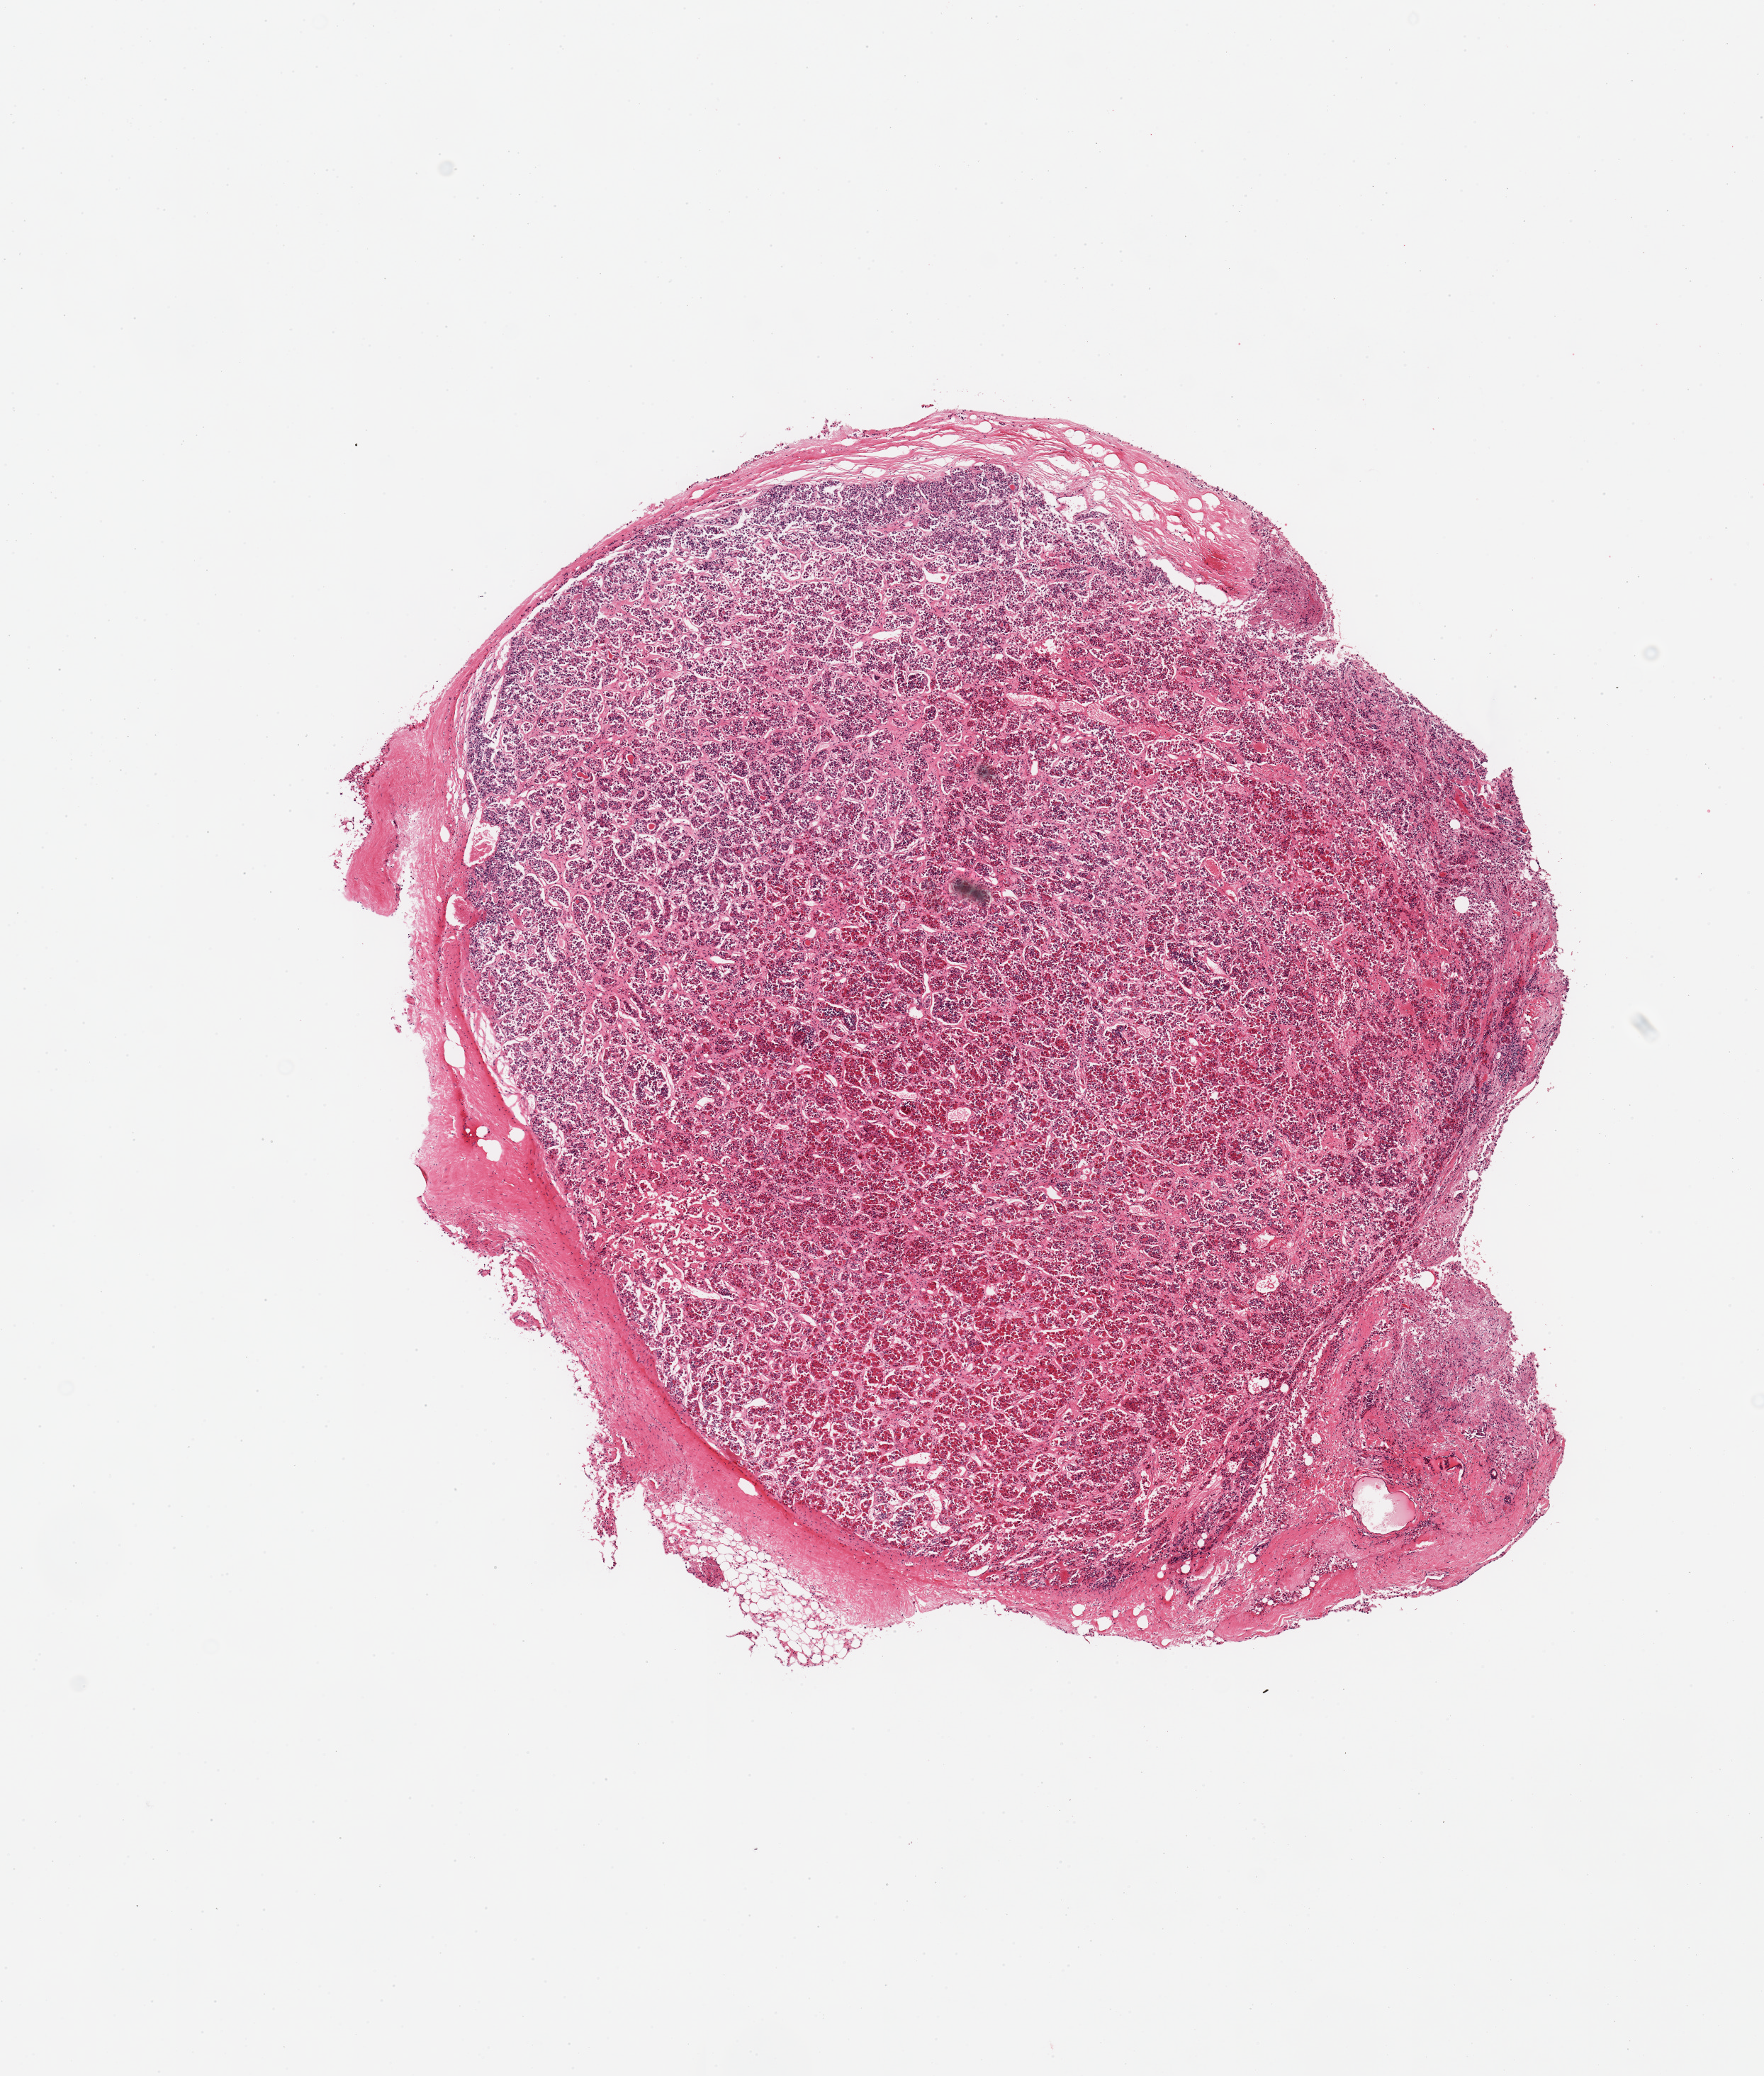
Digitized H&E-stained section — a low-resolution overview of the entire scanned area, about 9.8 x 11.6 mm (from a 20x scan); PAXgene-fixed, paraffin-embedded tissue; target tissue: pituitary; donor tissue sample.
Review note (as recorded): 1 piece; mostly adenohypophysis.